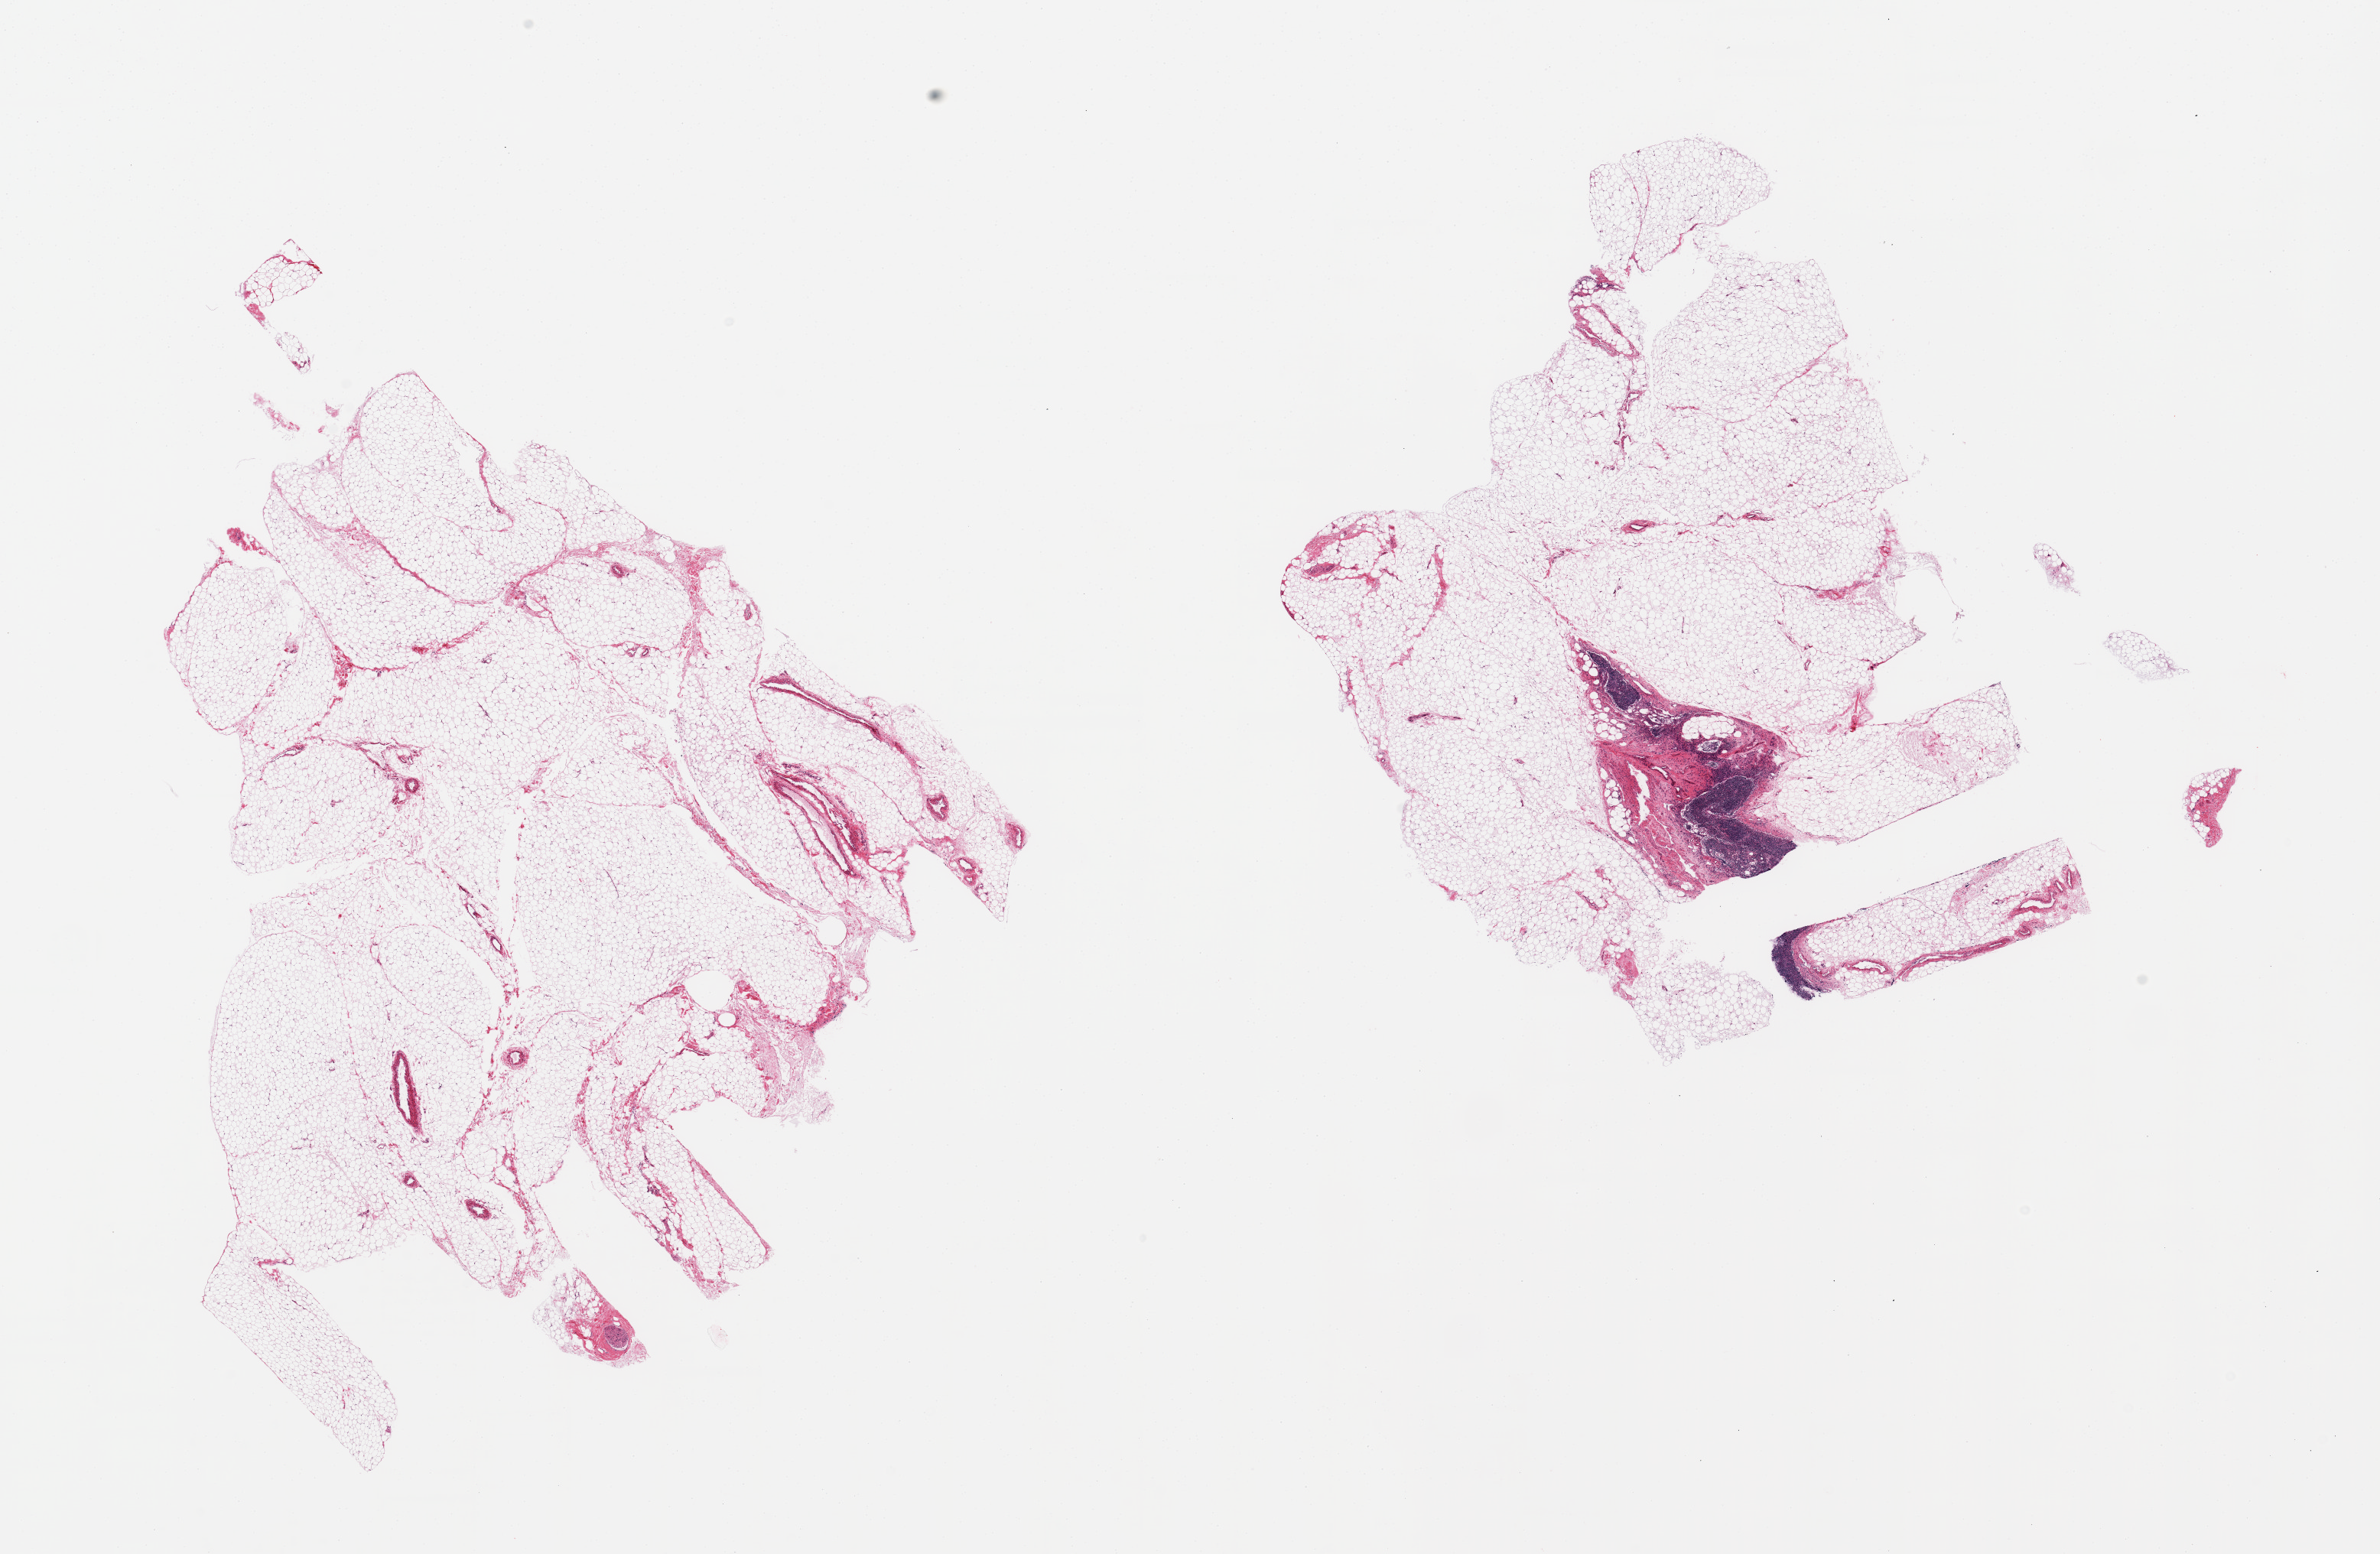
Whole-slide image, haematoxylin and eosin stain, whole scanned area (about 24.6 x 16.1 mm, slide scanned at 20x) shown as a low-resolution overview, PAXgene-fixed, paraffin-embedded tissue, section of omentum (target tissue), tissue donor sample. Donor sex: female.
* pathologist's review note for this sample: 2 pieces, incidental lymphoid aggregate; that and mesothelium are ~10-15% of tissue